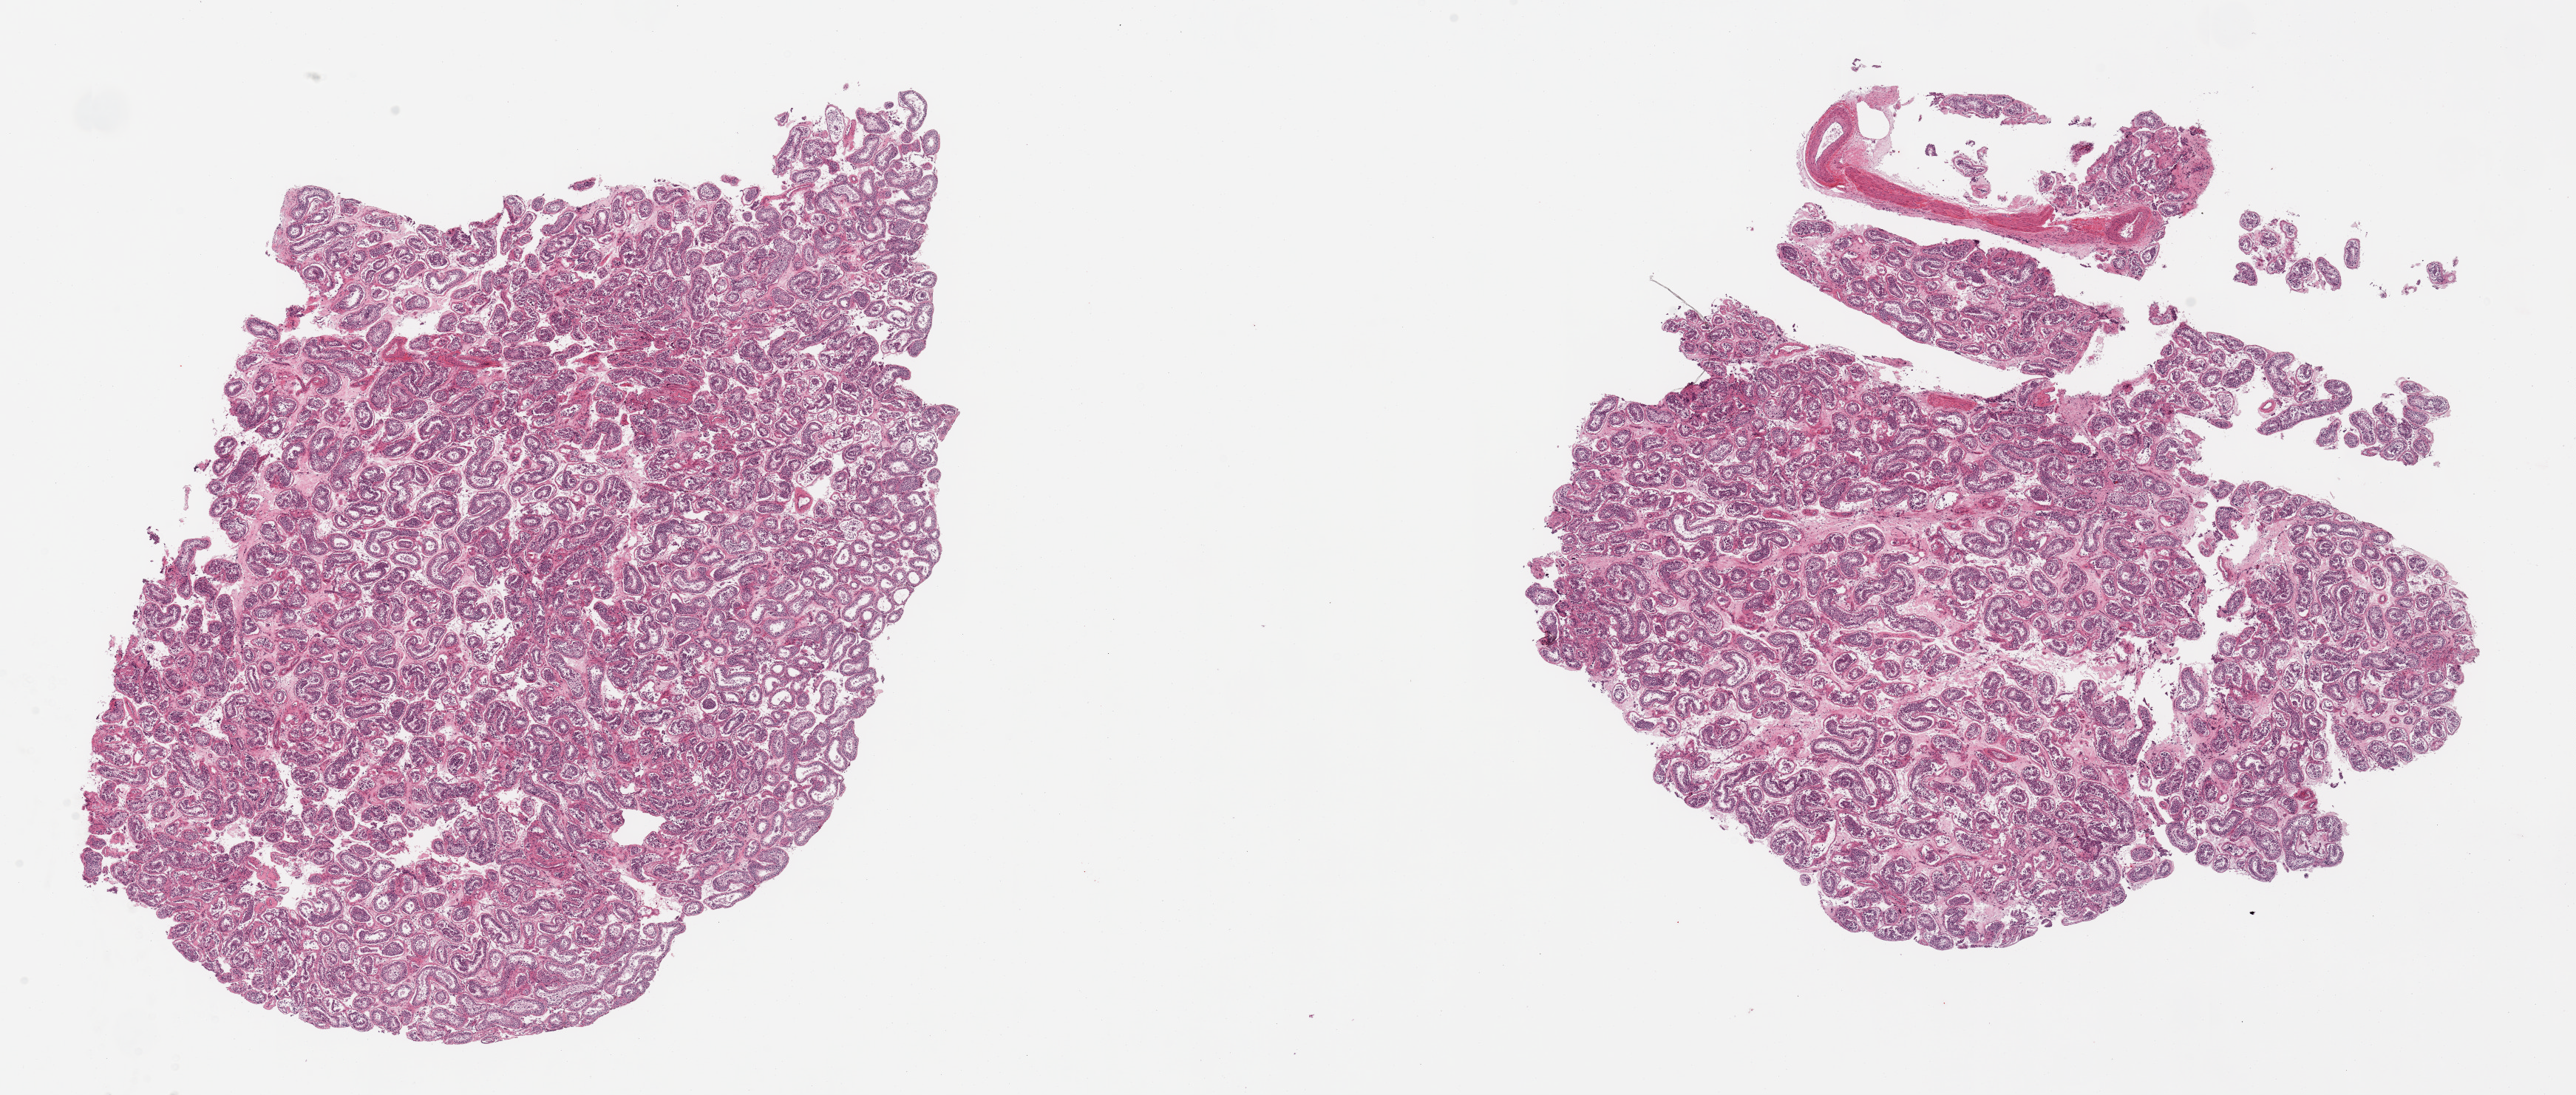
Digitized haematoxylin and eosin-stained section, brightfield, whole scanned area (about 27.6 x 11.7 mm) shown as a low-resolution overview, PAXgene-fixed paraffin-embedded (PFPE) section, sampled site (target tissue): testis, tissue donor sample. Male donor.
Review note (as recorded): 2 pieces; spermatogenesis is present.